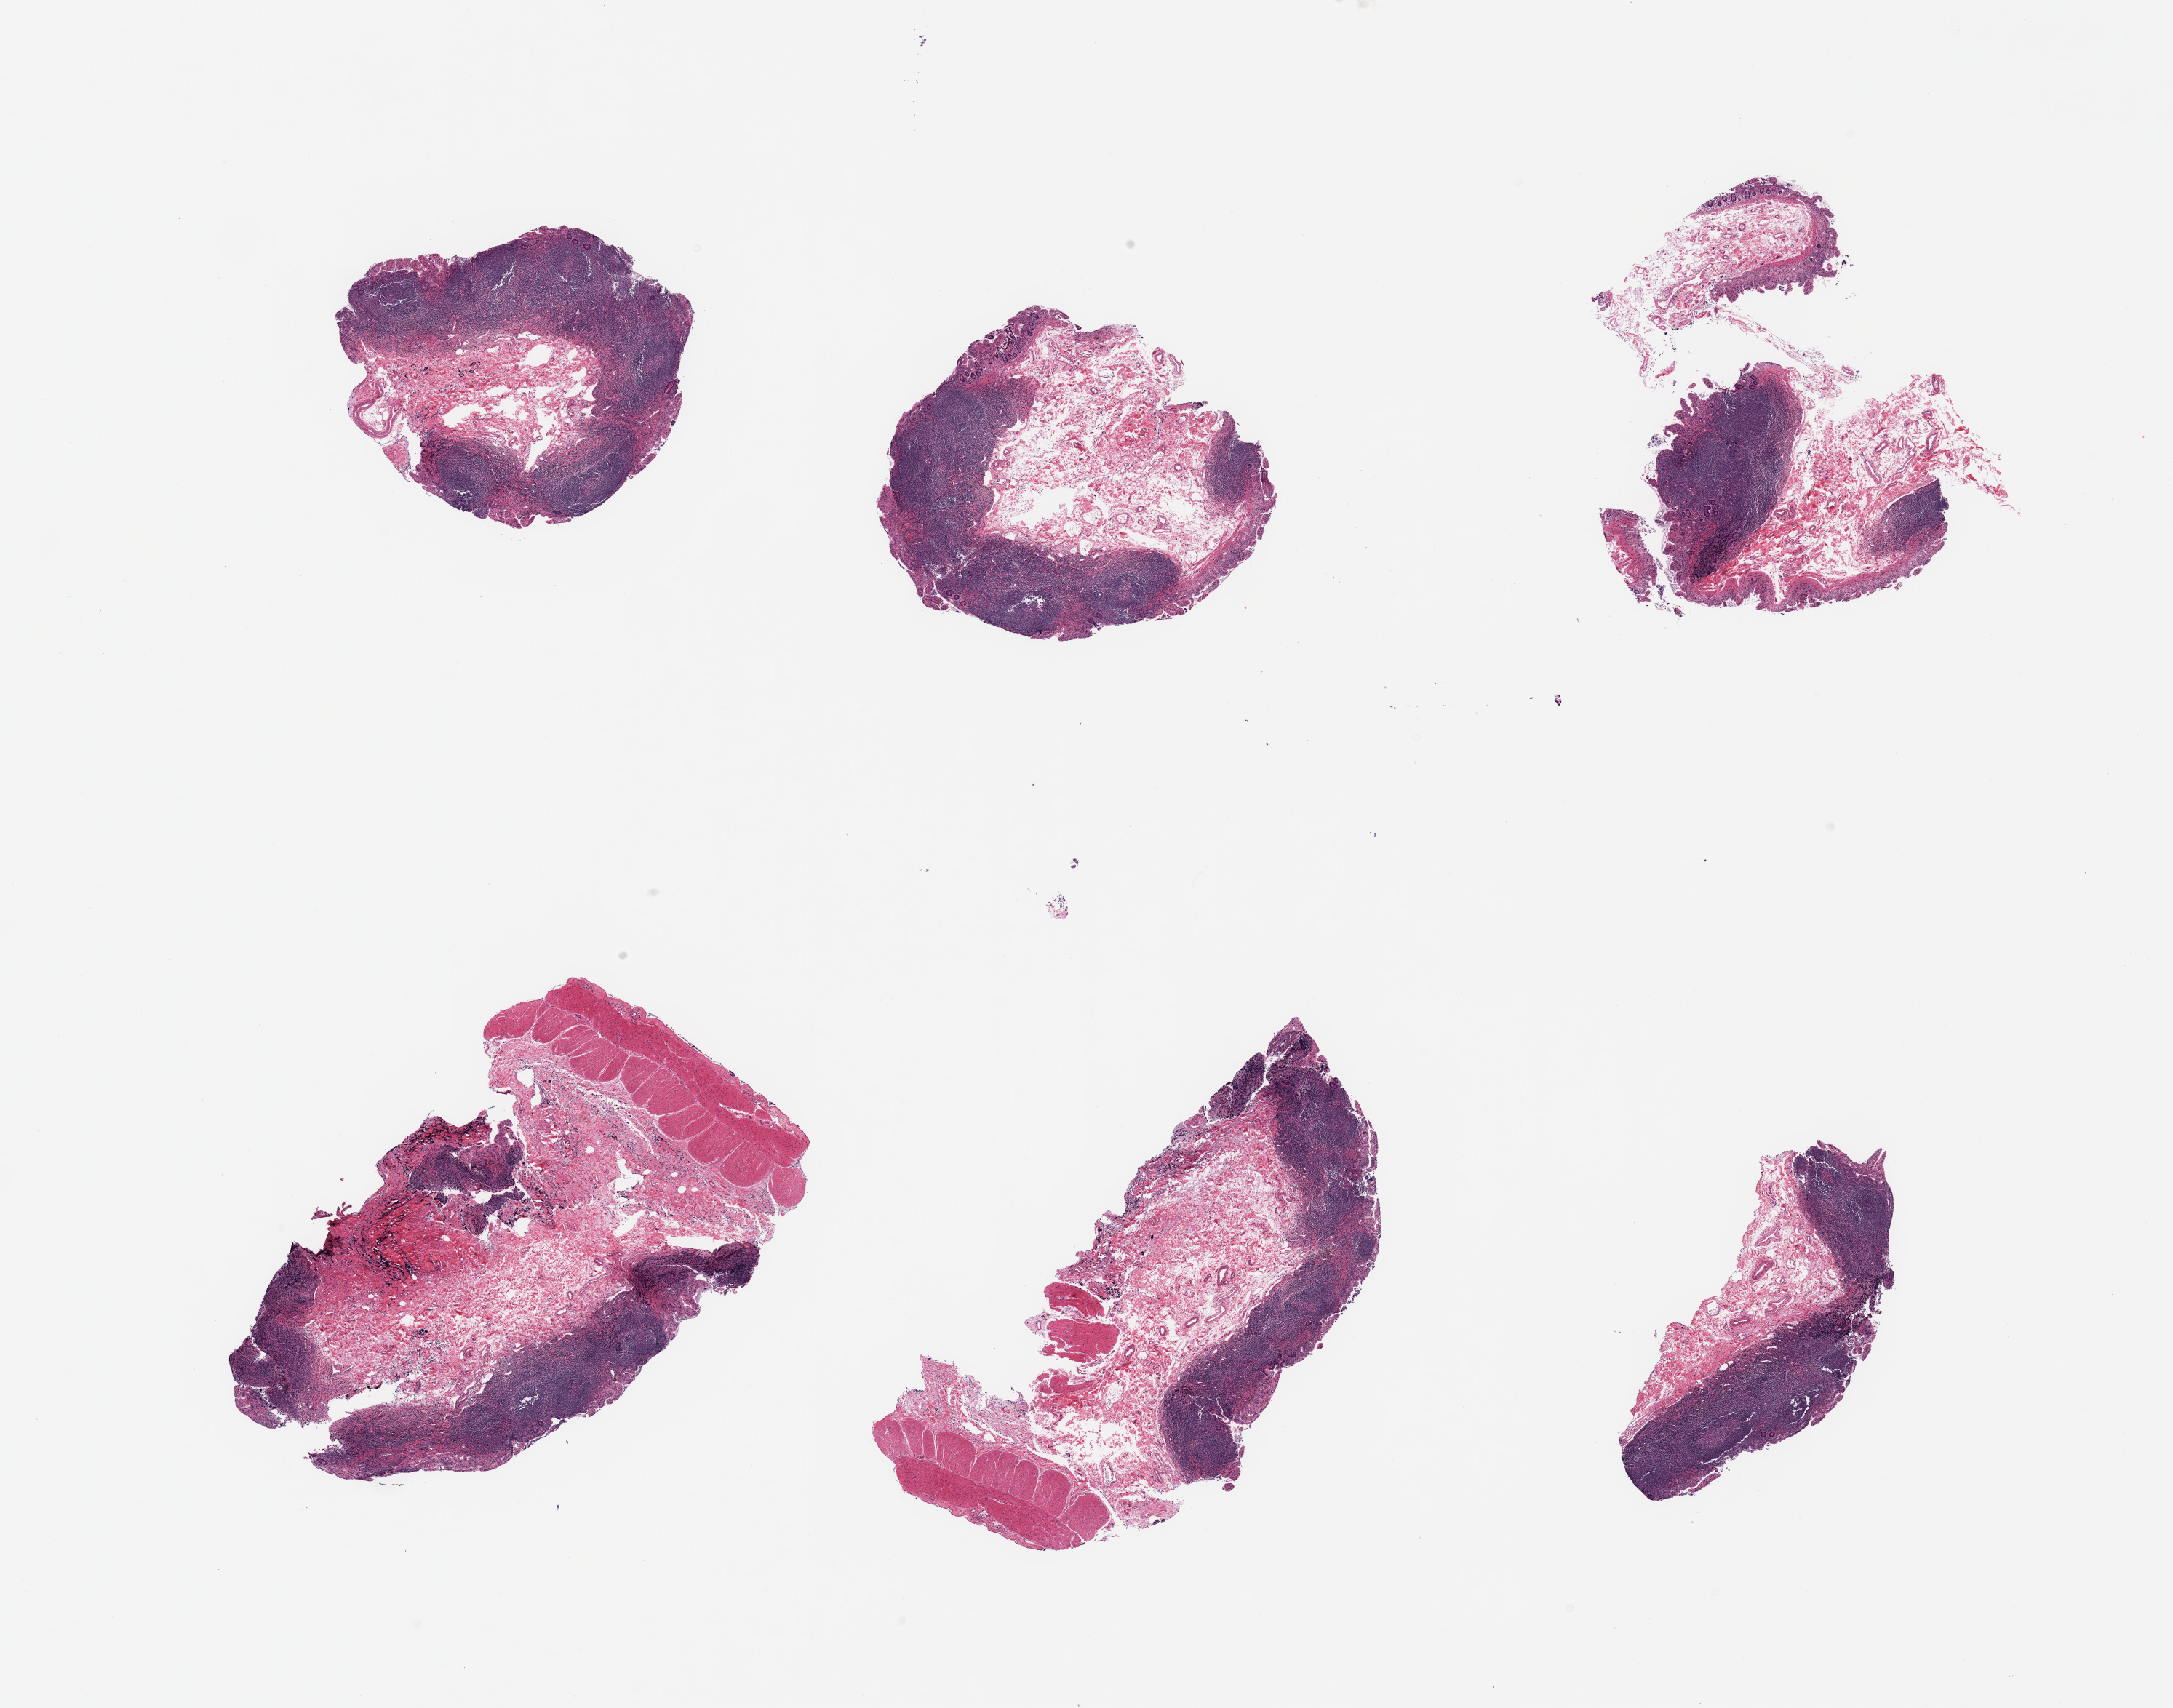
Whole-slide image, haematoxylin and eosin stain, whole scanned area (about 23.6 x 18.6 mm) shown as a low-resolution overview, PAXgene-fixed paraffin-embedded (PFPE) section, section of ileum (target tissue), donor tissue sample. Donor sex: female.
Review note (as recorded): 6 pieces, ~30% target lymphoid aggregates, well preserved, excellent specimen.